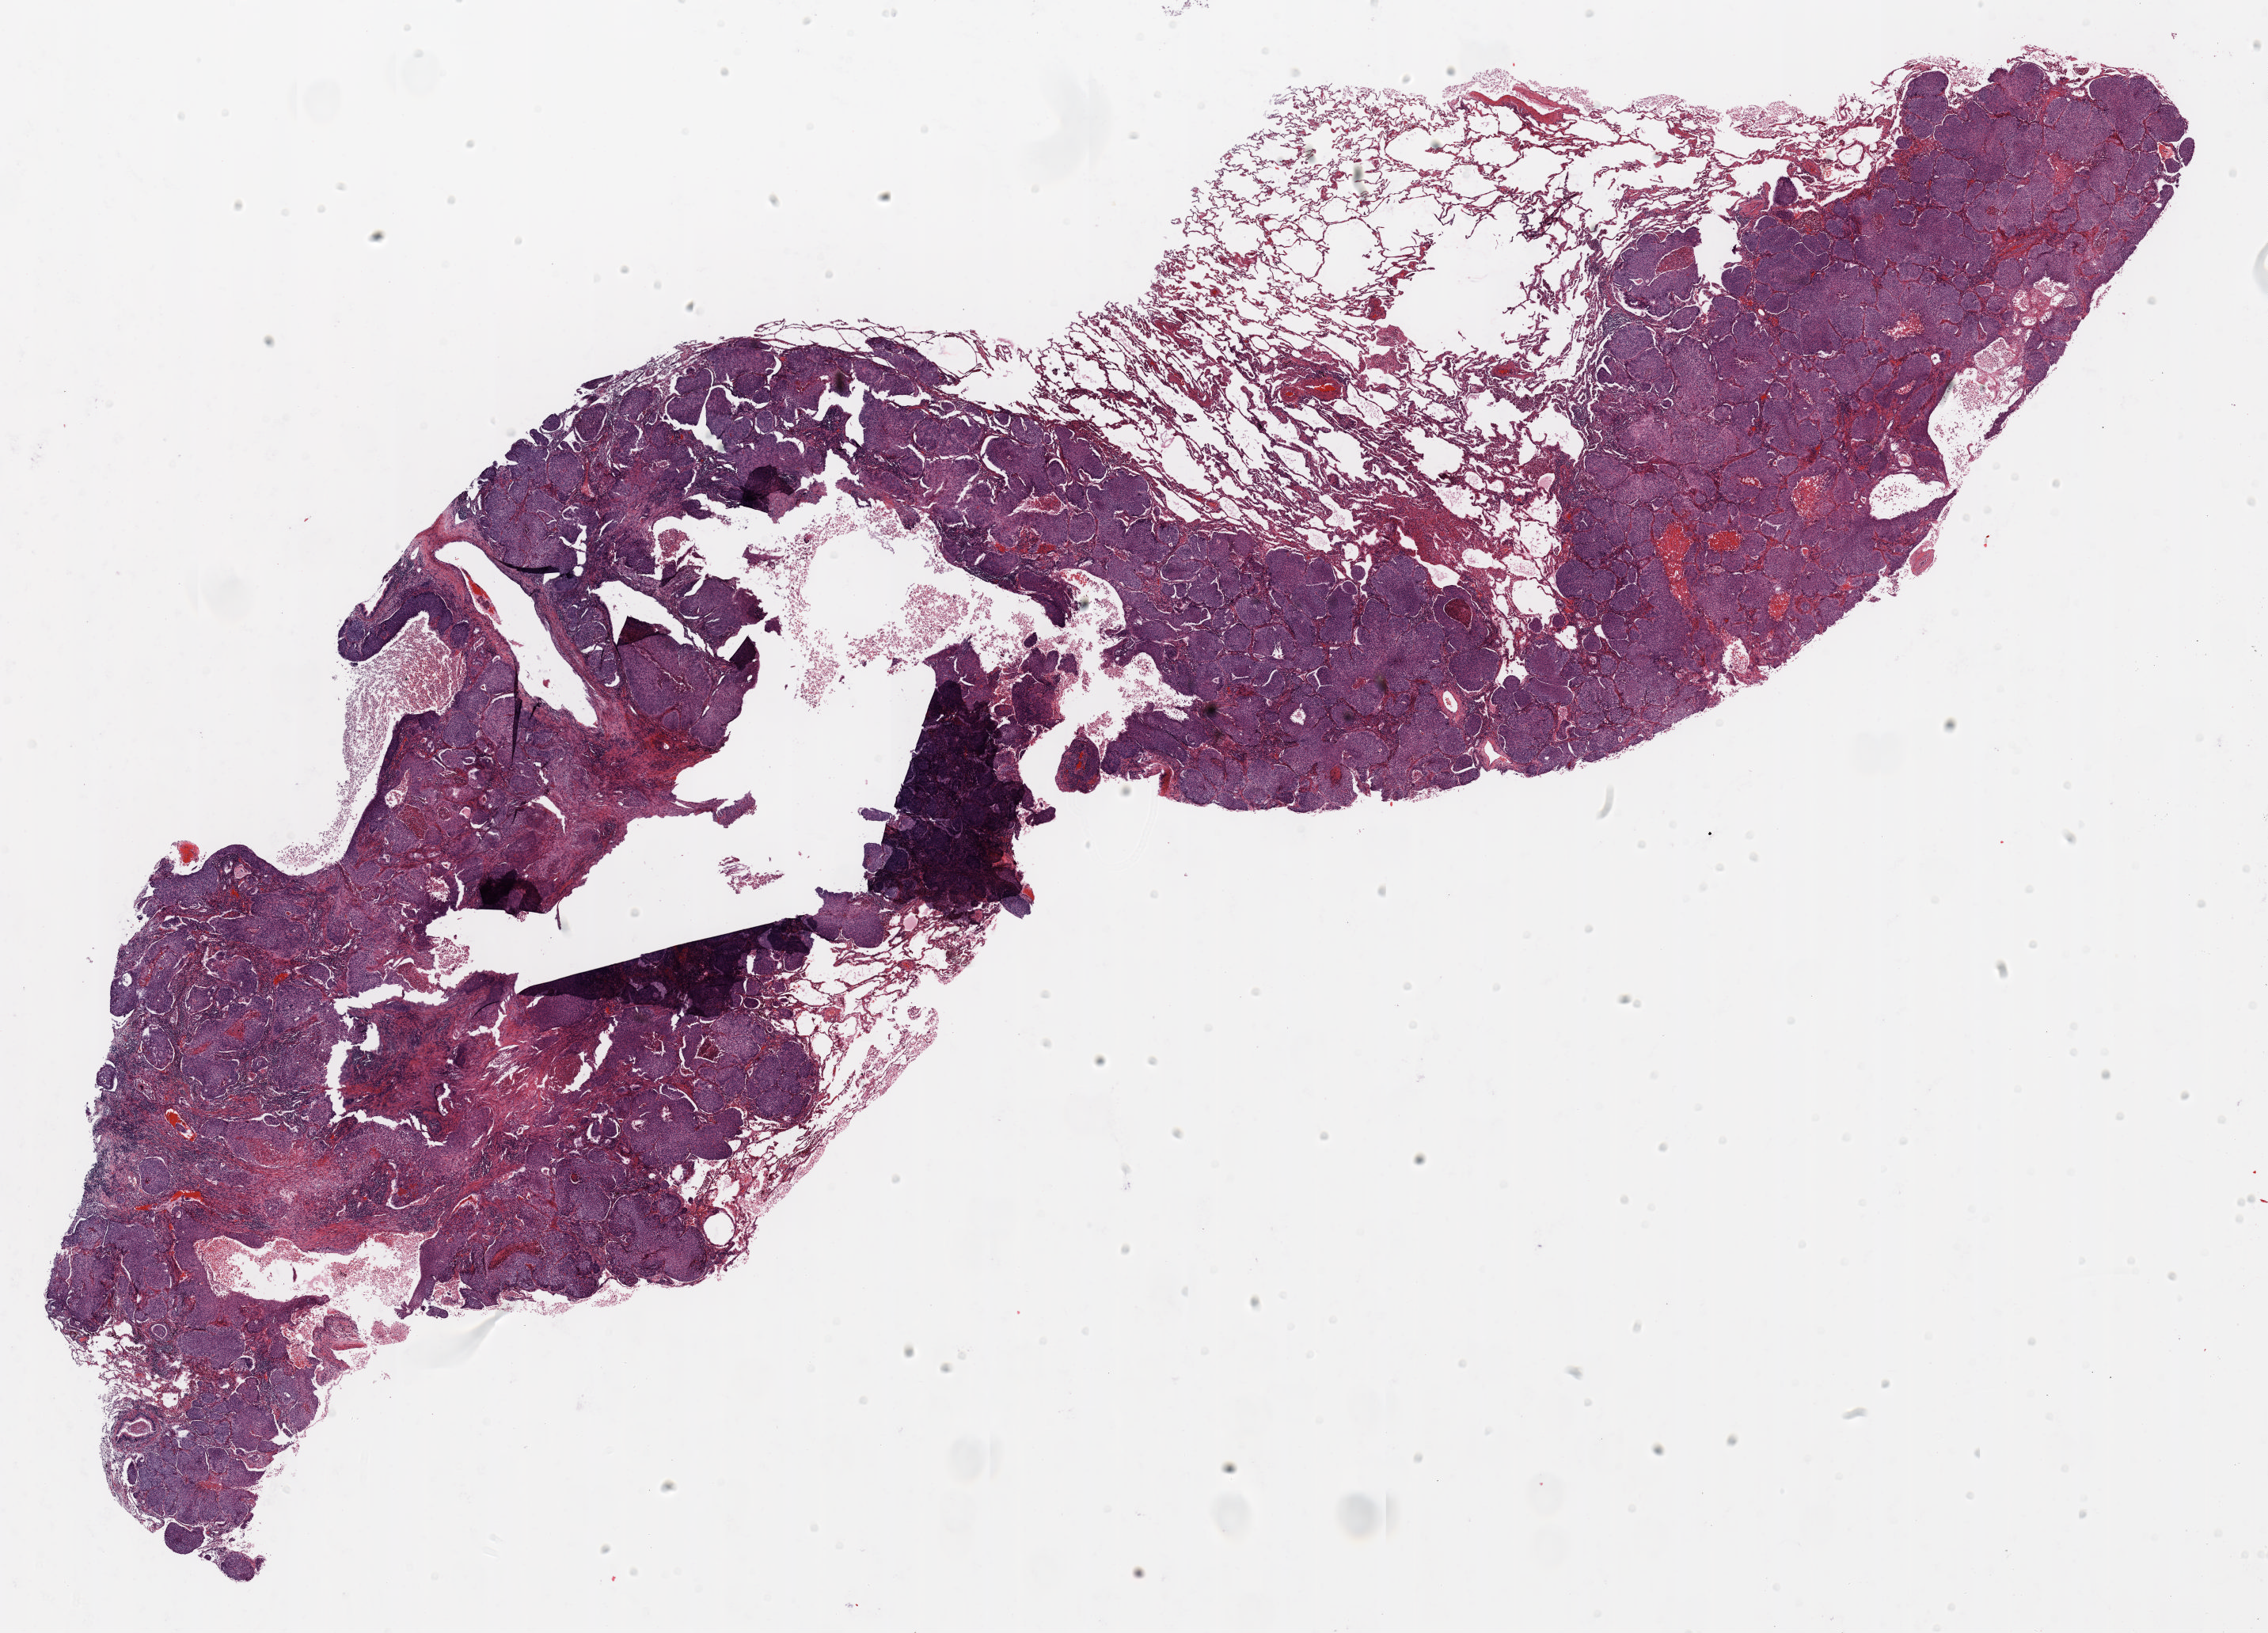
Whole-slide histology image, H&E-stained — low-resolution overview of the scanned area, about 23.0 x 16.6 mm, FFPE section, lung tissue. Female, age 59 at enrolment. Former smoker at enrolment. Grade: moderately differentiated (G2).
* participant's lung-cancer diagnosis: Squamous cell carcinoma, NOS
* primary tumour location (clinical record): right lower lobe
* tumour size (pathology): 13 mm
* stage (AJCC 6th edition): IA